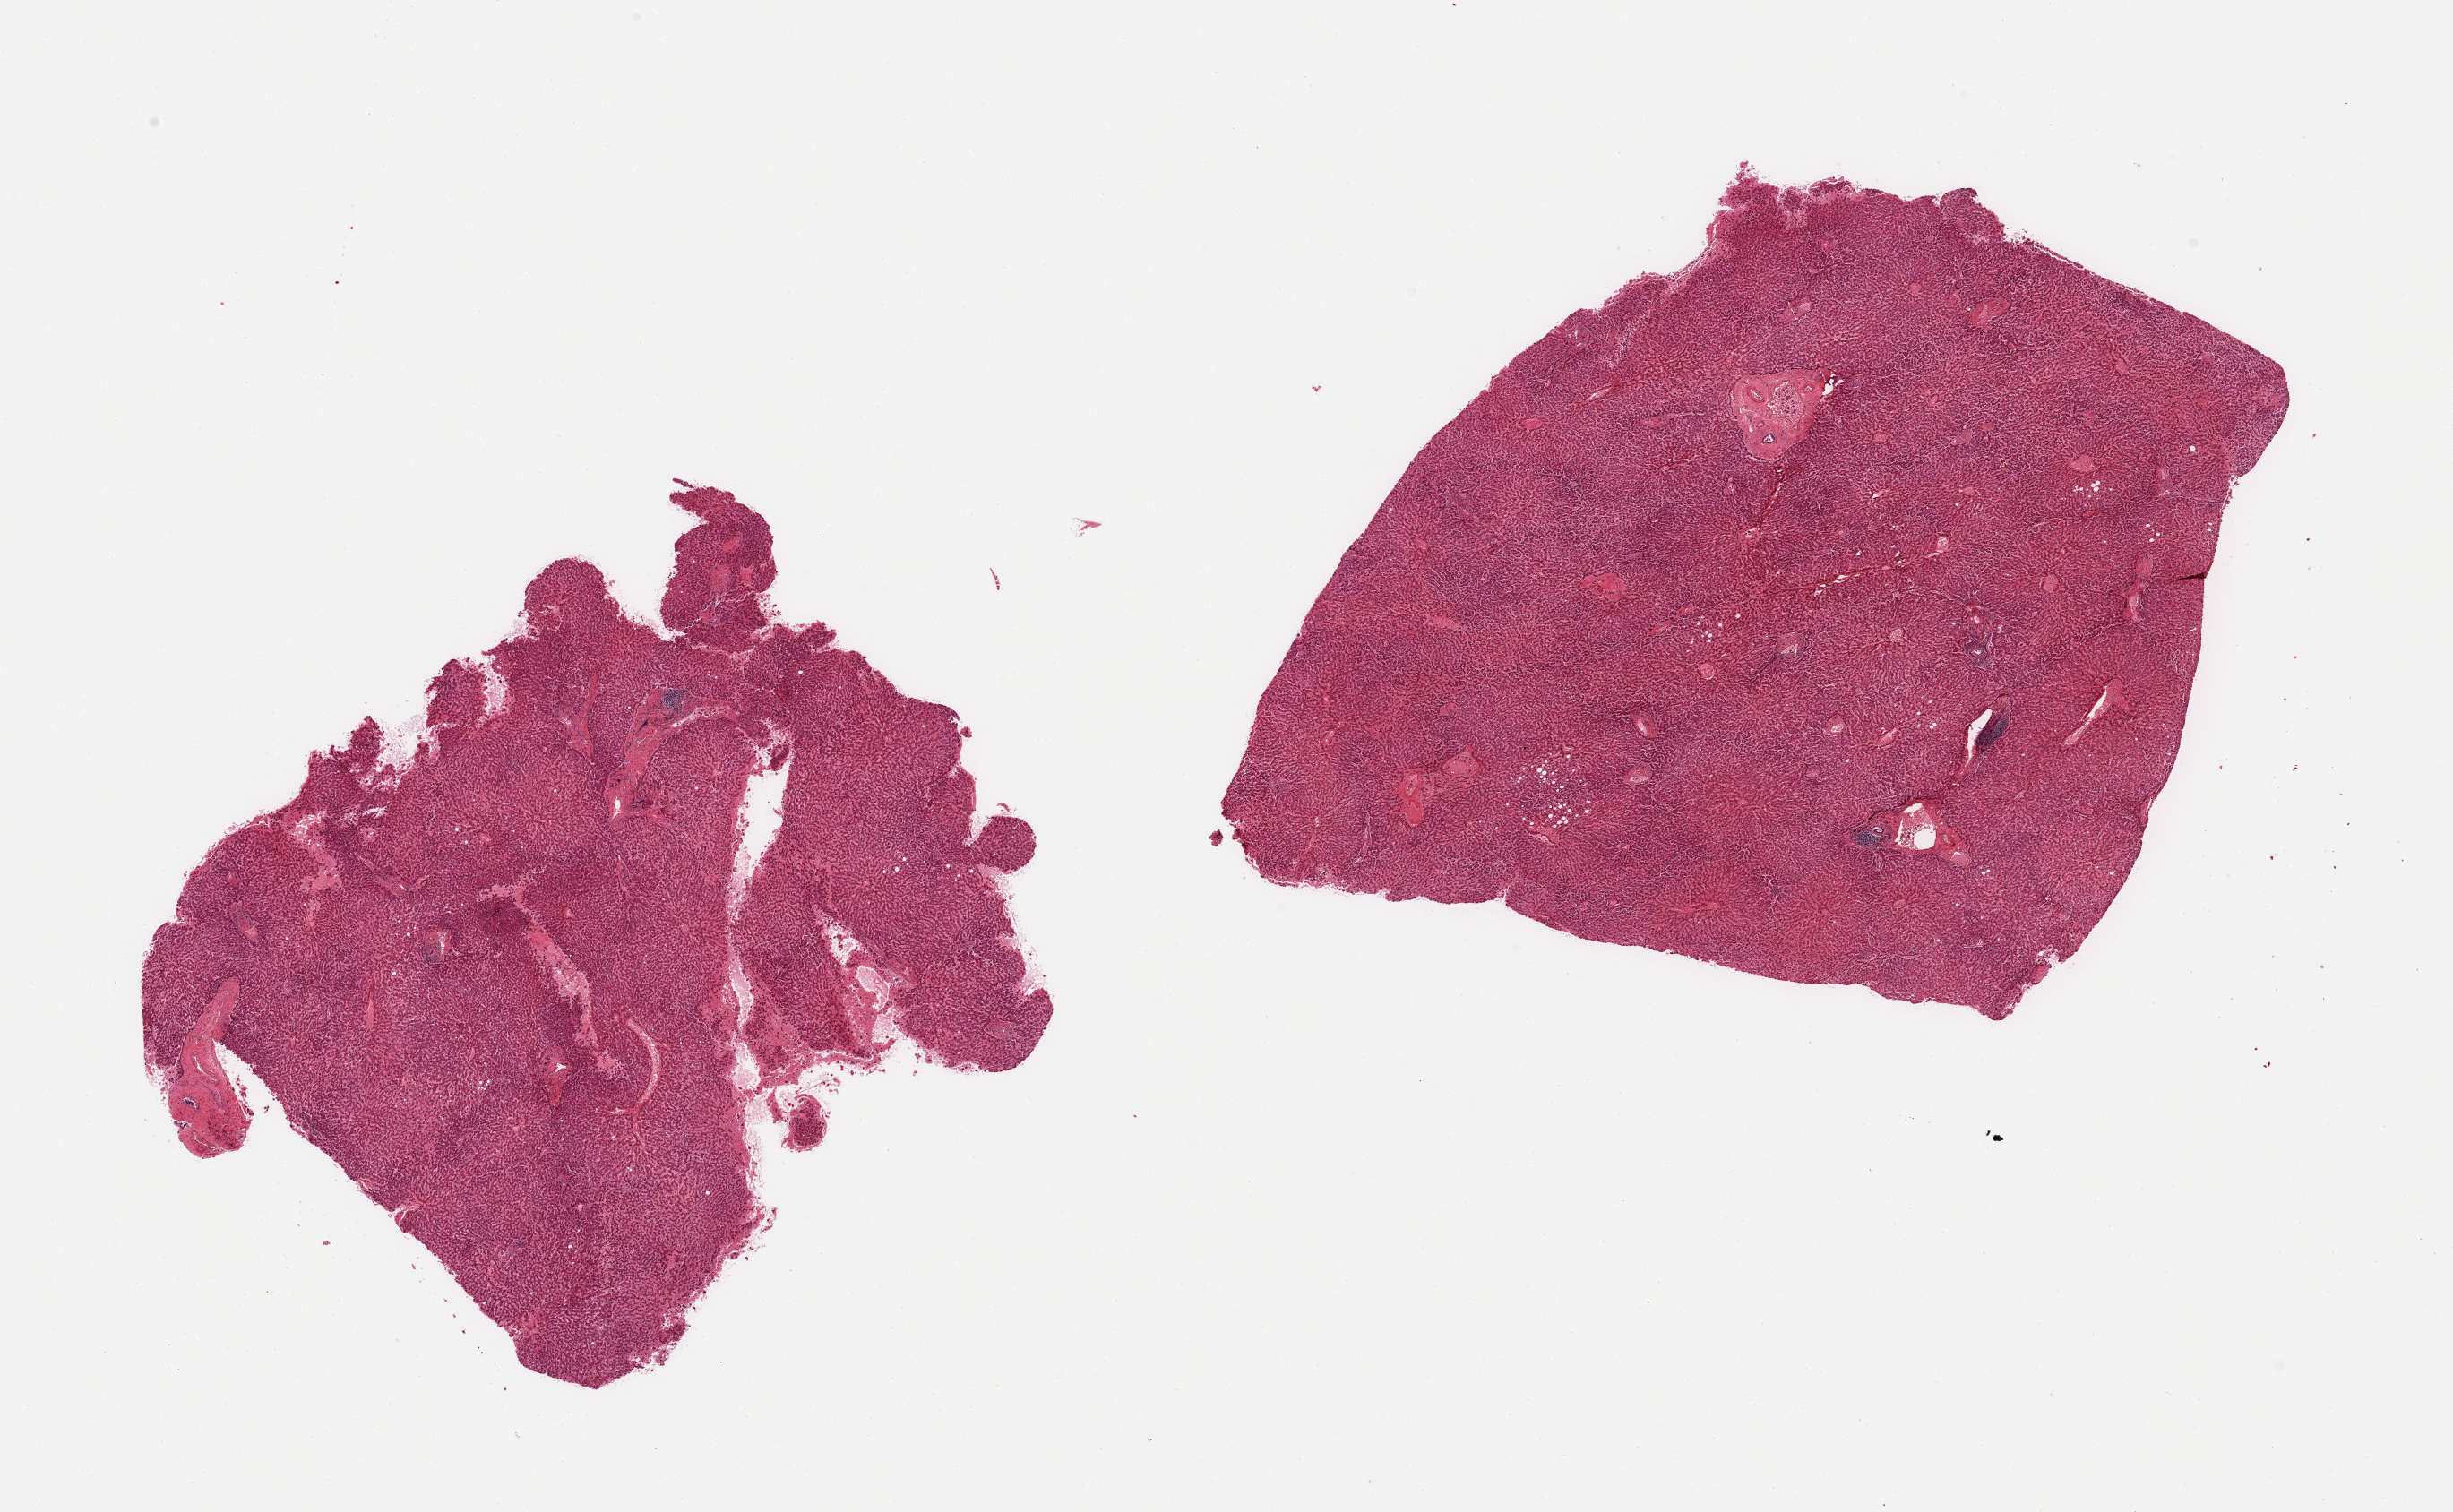
Whole-slide image, haematoxylin and eosin stain, low-resolution overview of the scanned area, about 21.7 x 13.4 mm, PAXgene-fixed, paraffin-embedded tissue, sampled site (target tissue): liver, donor tissue sample.
* reviewer comment on this tissue sample: 2 pieces, moderate chronic passsive congestion